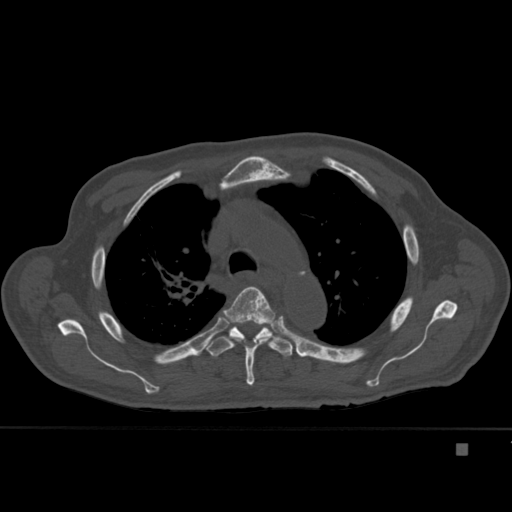
CT including the spine, one axial slice; position 315 of 451 along the scan axis; bone window (W 1800 / L 400 HU); 1.5 mm slice thickness; 512 × 512 image matrix, field of view 378 × 378 mm. Patient: male, 75 years. Case-level facts recorded for this patient, not image findings: primary cancer: prostate.
Outlined on this slice (semi-automatic segmentation, software-assisted and operator-edited):
- T4 vertebra: bounding box <223,287,279,386> (left, top, right, bottom; pixels)
- T5 vertebra: <206,323,293,357>